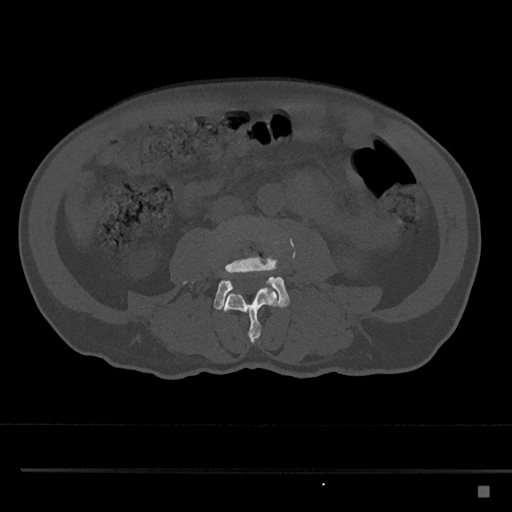
CT including the spine, one axial slice; slice 666 of 797 in the series (ordered by position); reconstruction kernel Br40s/3; 120 kVp; bone window (W 1800 / L 400 HU); 0.5 mm slice thickness; 512 × 512 image matrix, field of view 391 × 391 mm. Patient: male, 59 years. From the clinical record (not read from this slice): primary cancer: prostate.
Outlined on this slice (semi-automatic segmentation, software-assisted and operator-edited):
- L3 vertebra: bounding box [x1, y1, x2, y2] px = [220, 282, 281, 343]
- L4 vertebra: [183, 235, 290, 310]